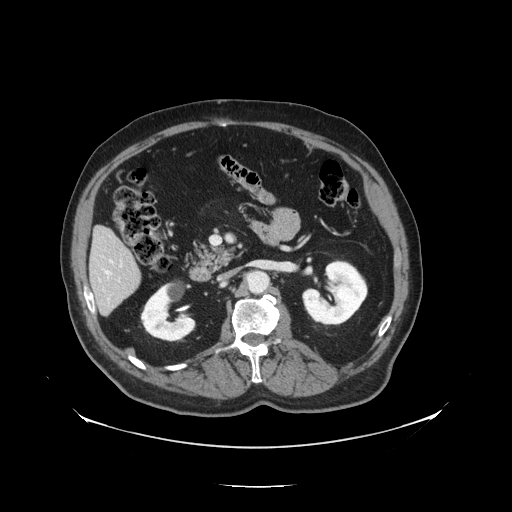
Contrast-enhanced abdominal CT, one axial slice; position 56 of 138 along the scan axis; reconstruction kernel STANDARD; 120 kVp; soft-tissue window (W 400 / L 40 HU); 512 × 512 image matrix, field of view 497 × 497 mm. Male patient, age 77 years. Case-level facts recorded for this patient, not image findings: diagnosis: colorectal cancer liver metastases, imaged before liver resection; multiple liver metastases: no; largest metastasis: 1.5 cm.
Outlined on this slice (outlined manually by an expert reader):
- liver: bounding box <91,229,141,313> (left, top, right, bottom; pixels)
- planned liver remnant (the part of the liver to remain after resection): <92,229,138,283>